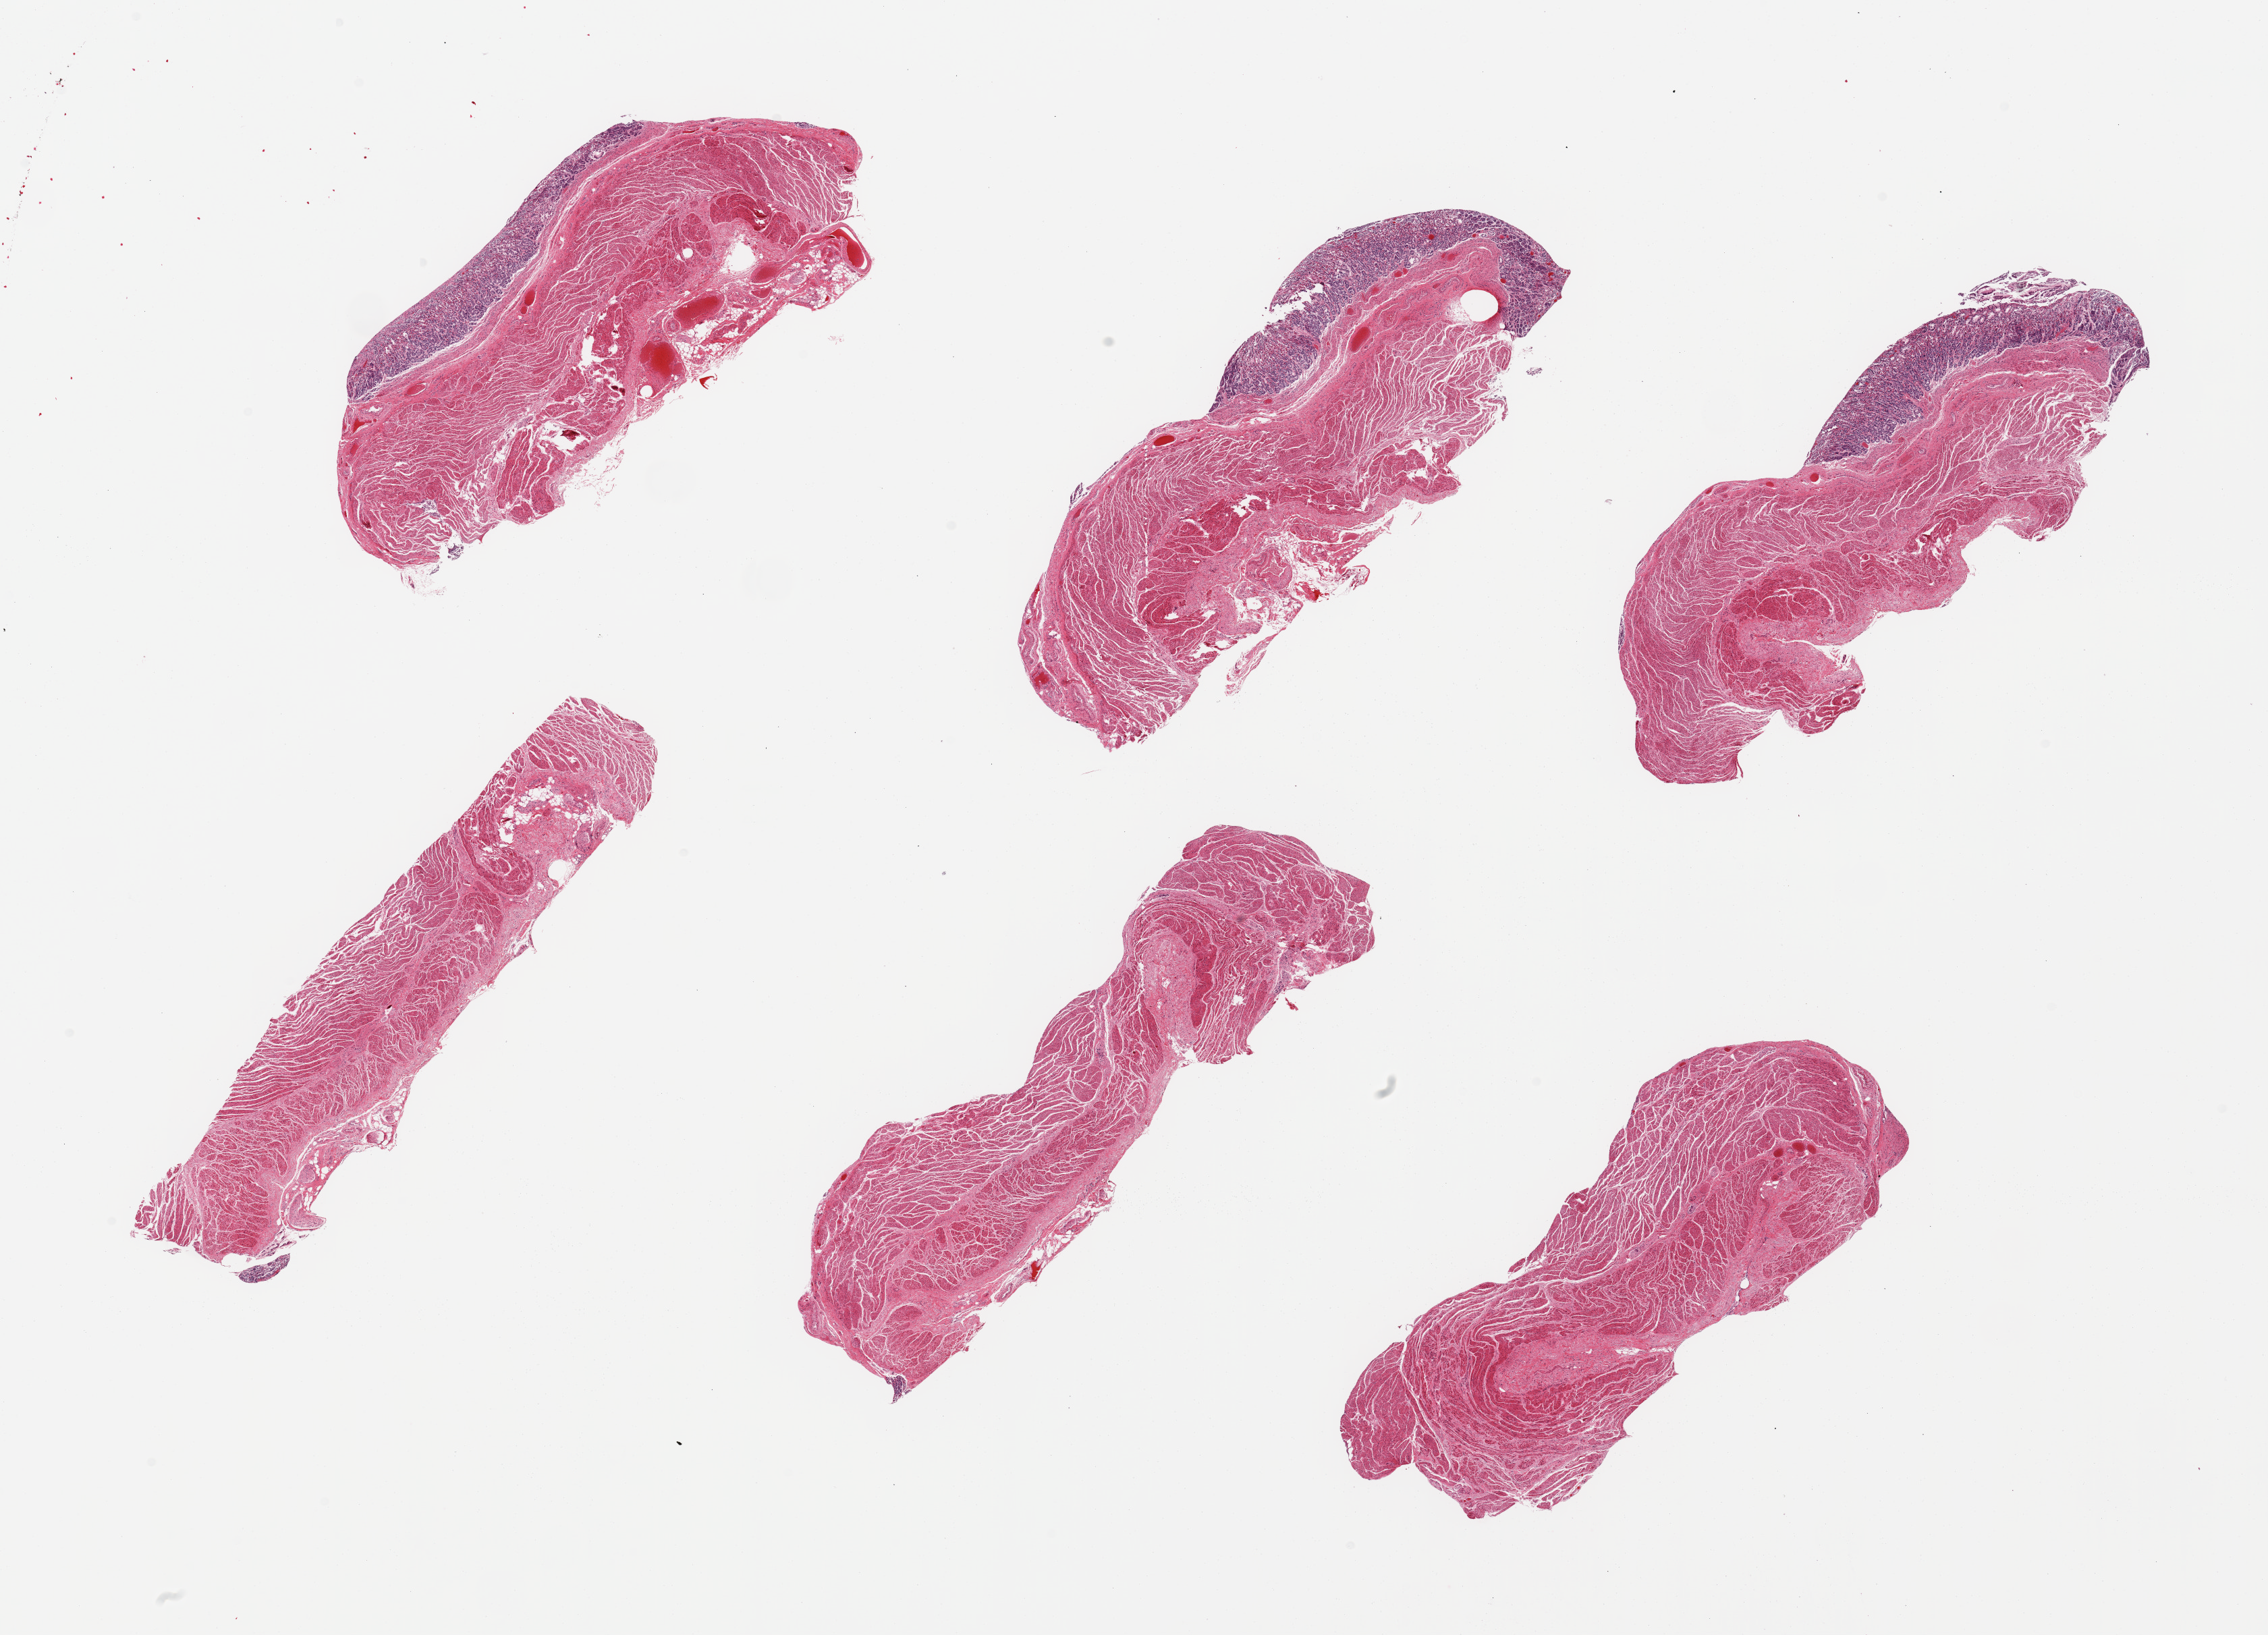
H&E whole-slide image, low-resolution overview of the scanned area, about 26.6 x 19.2 mm (slide scanned at 20x). PAXgene-fixed paraffin-embedded (PFPE) section. Target tissue: gastroesophageal junction. Tissue donor sample.
Review note (as recorded): 6 pieces; 3 of 6 contain gastric mucosa (not target) in addition to muscularis (target).